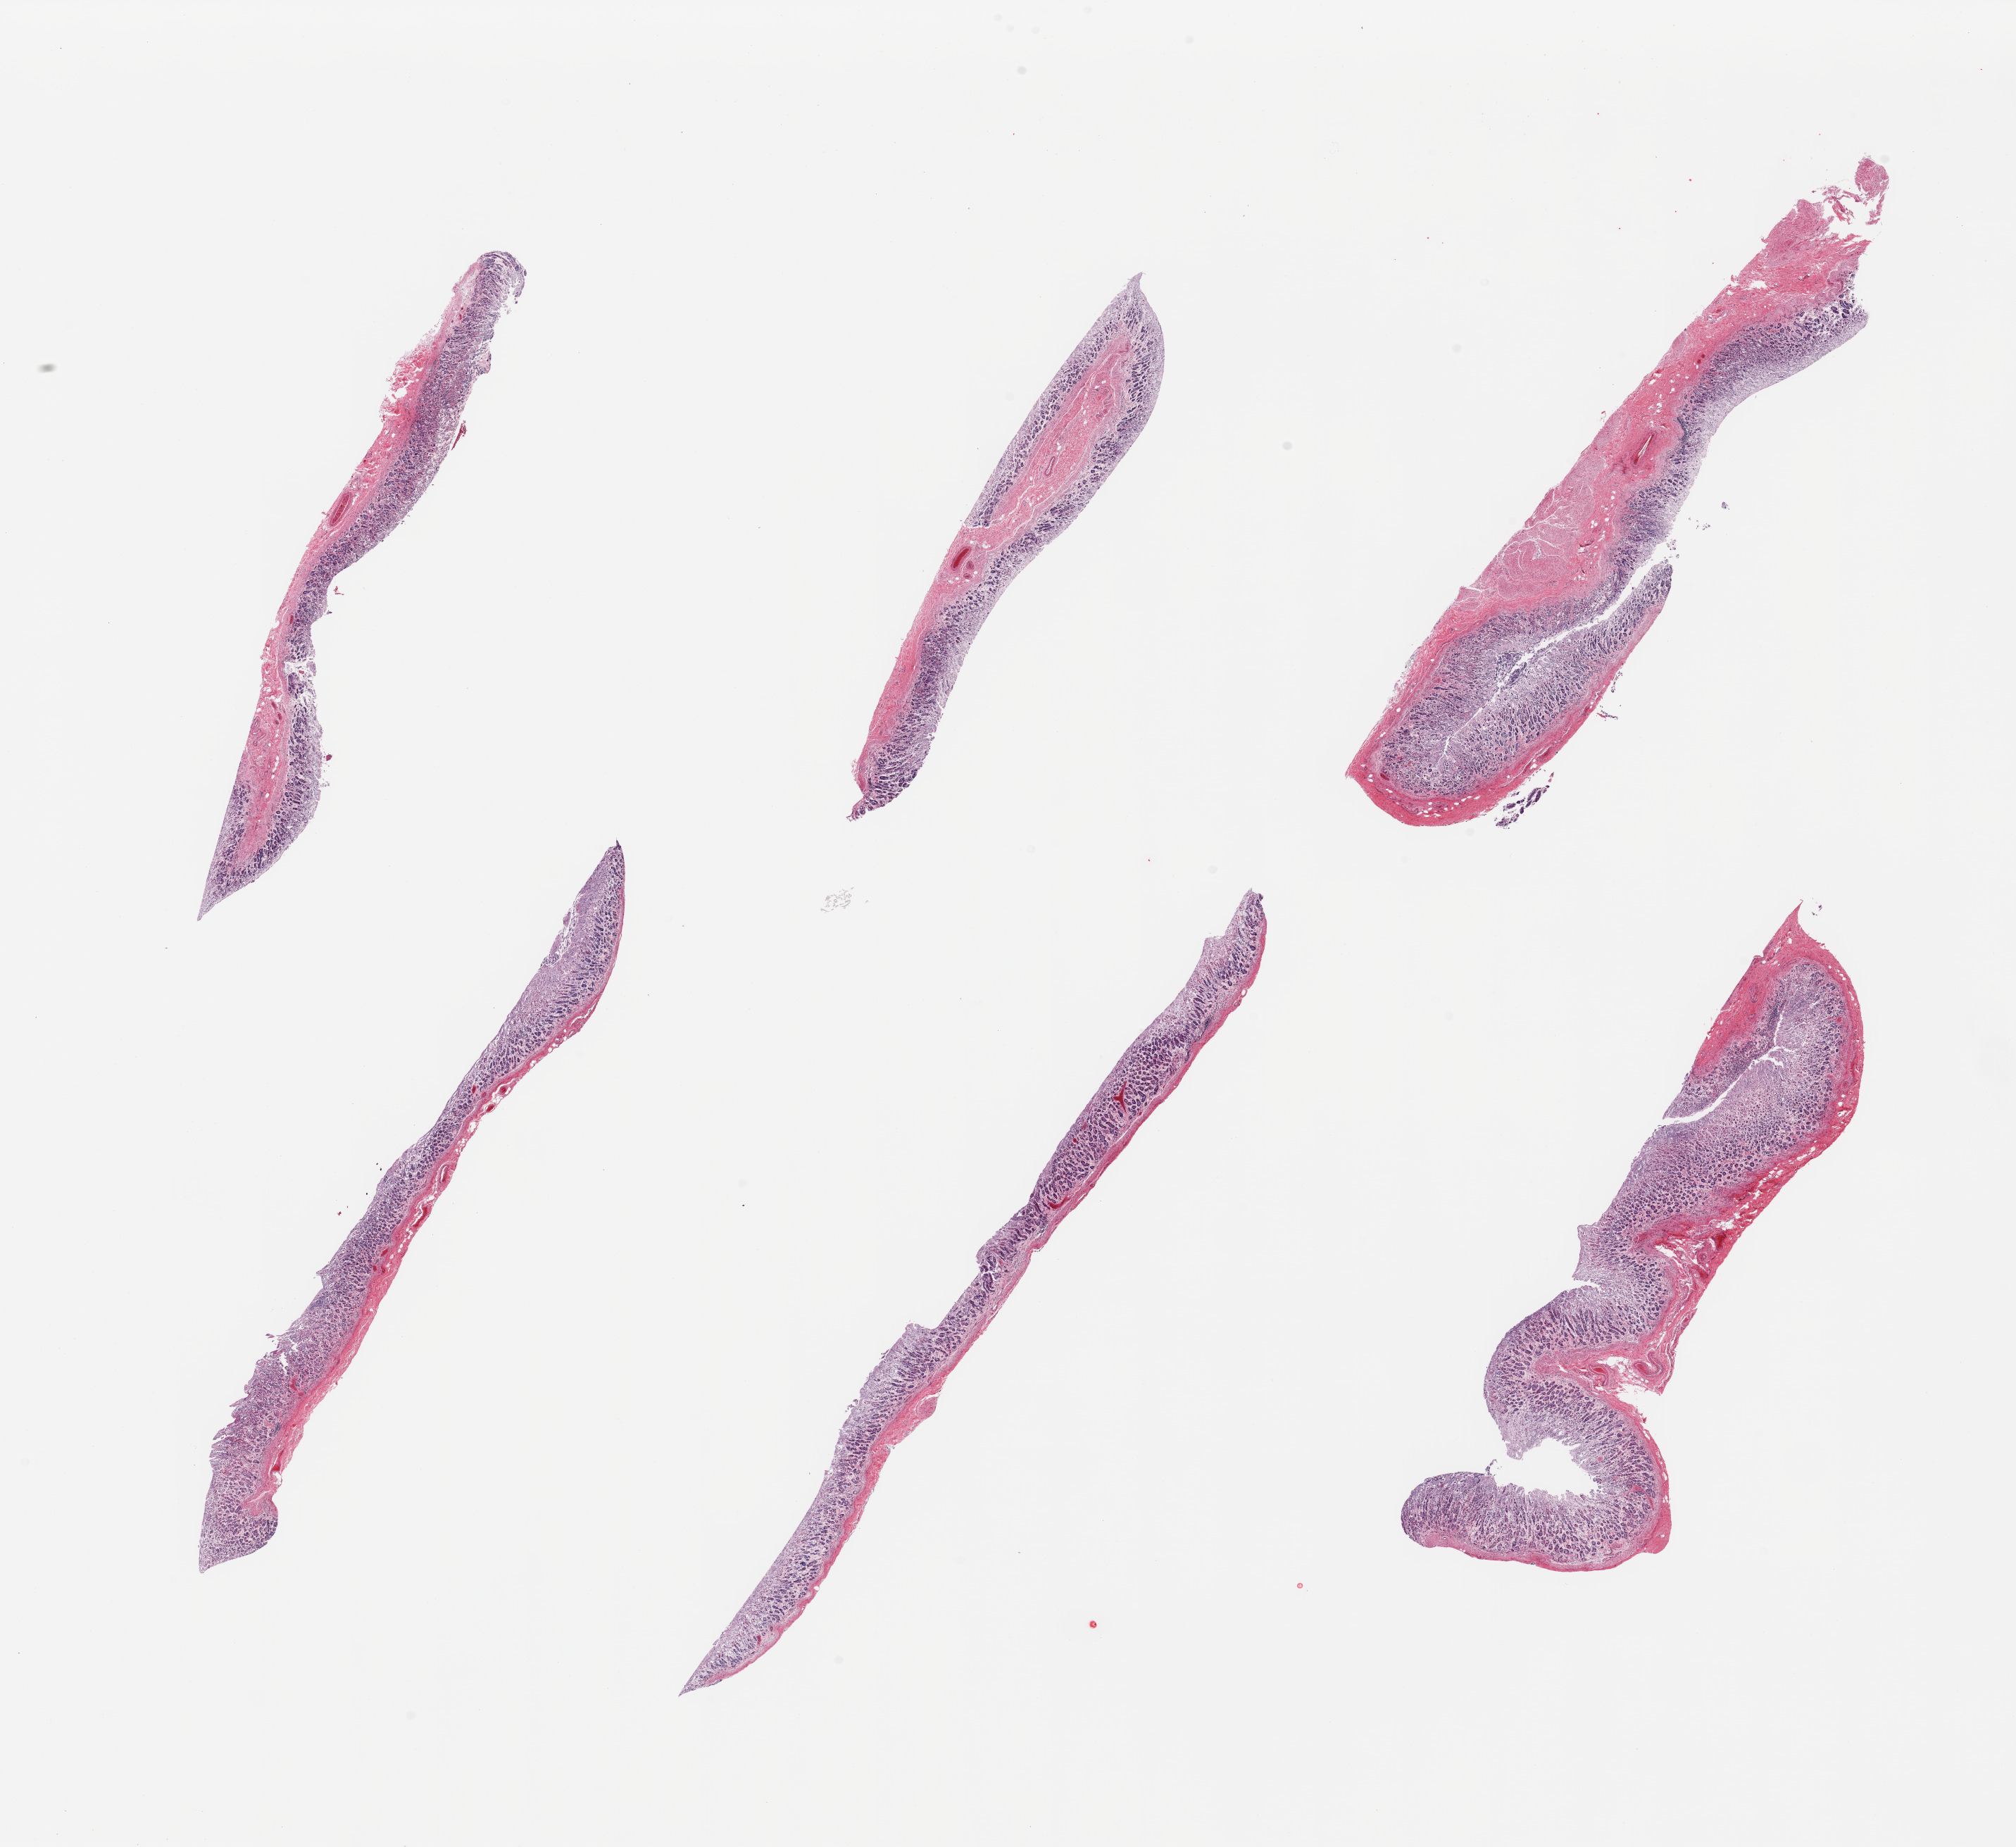
Digitized hematoxylin and eosin (H&E)-stained section, whole scanned area (about 22.6 x 20.7 mm, slide scanned at 20x) shown as a low-resolution overview. PAXgene-fixed, paraffin-embedded tissue. Sampled site (target tissue): stomach. Tissue donor sample. Female donor.
* reviewer comment on this tissue sample: 6 pieces; mucosa severely autolyzed; no muscularis included